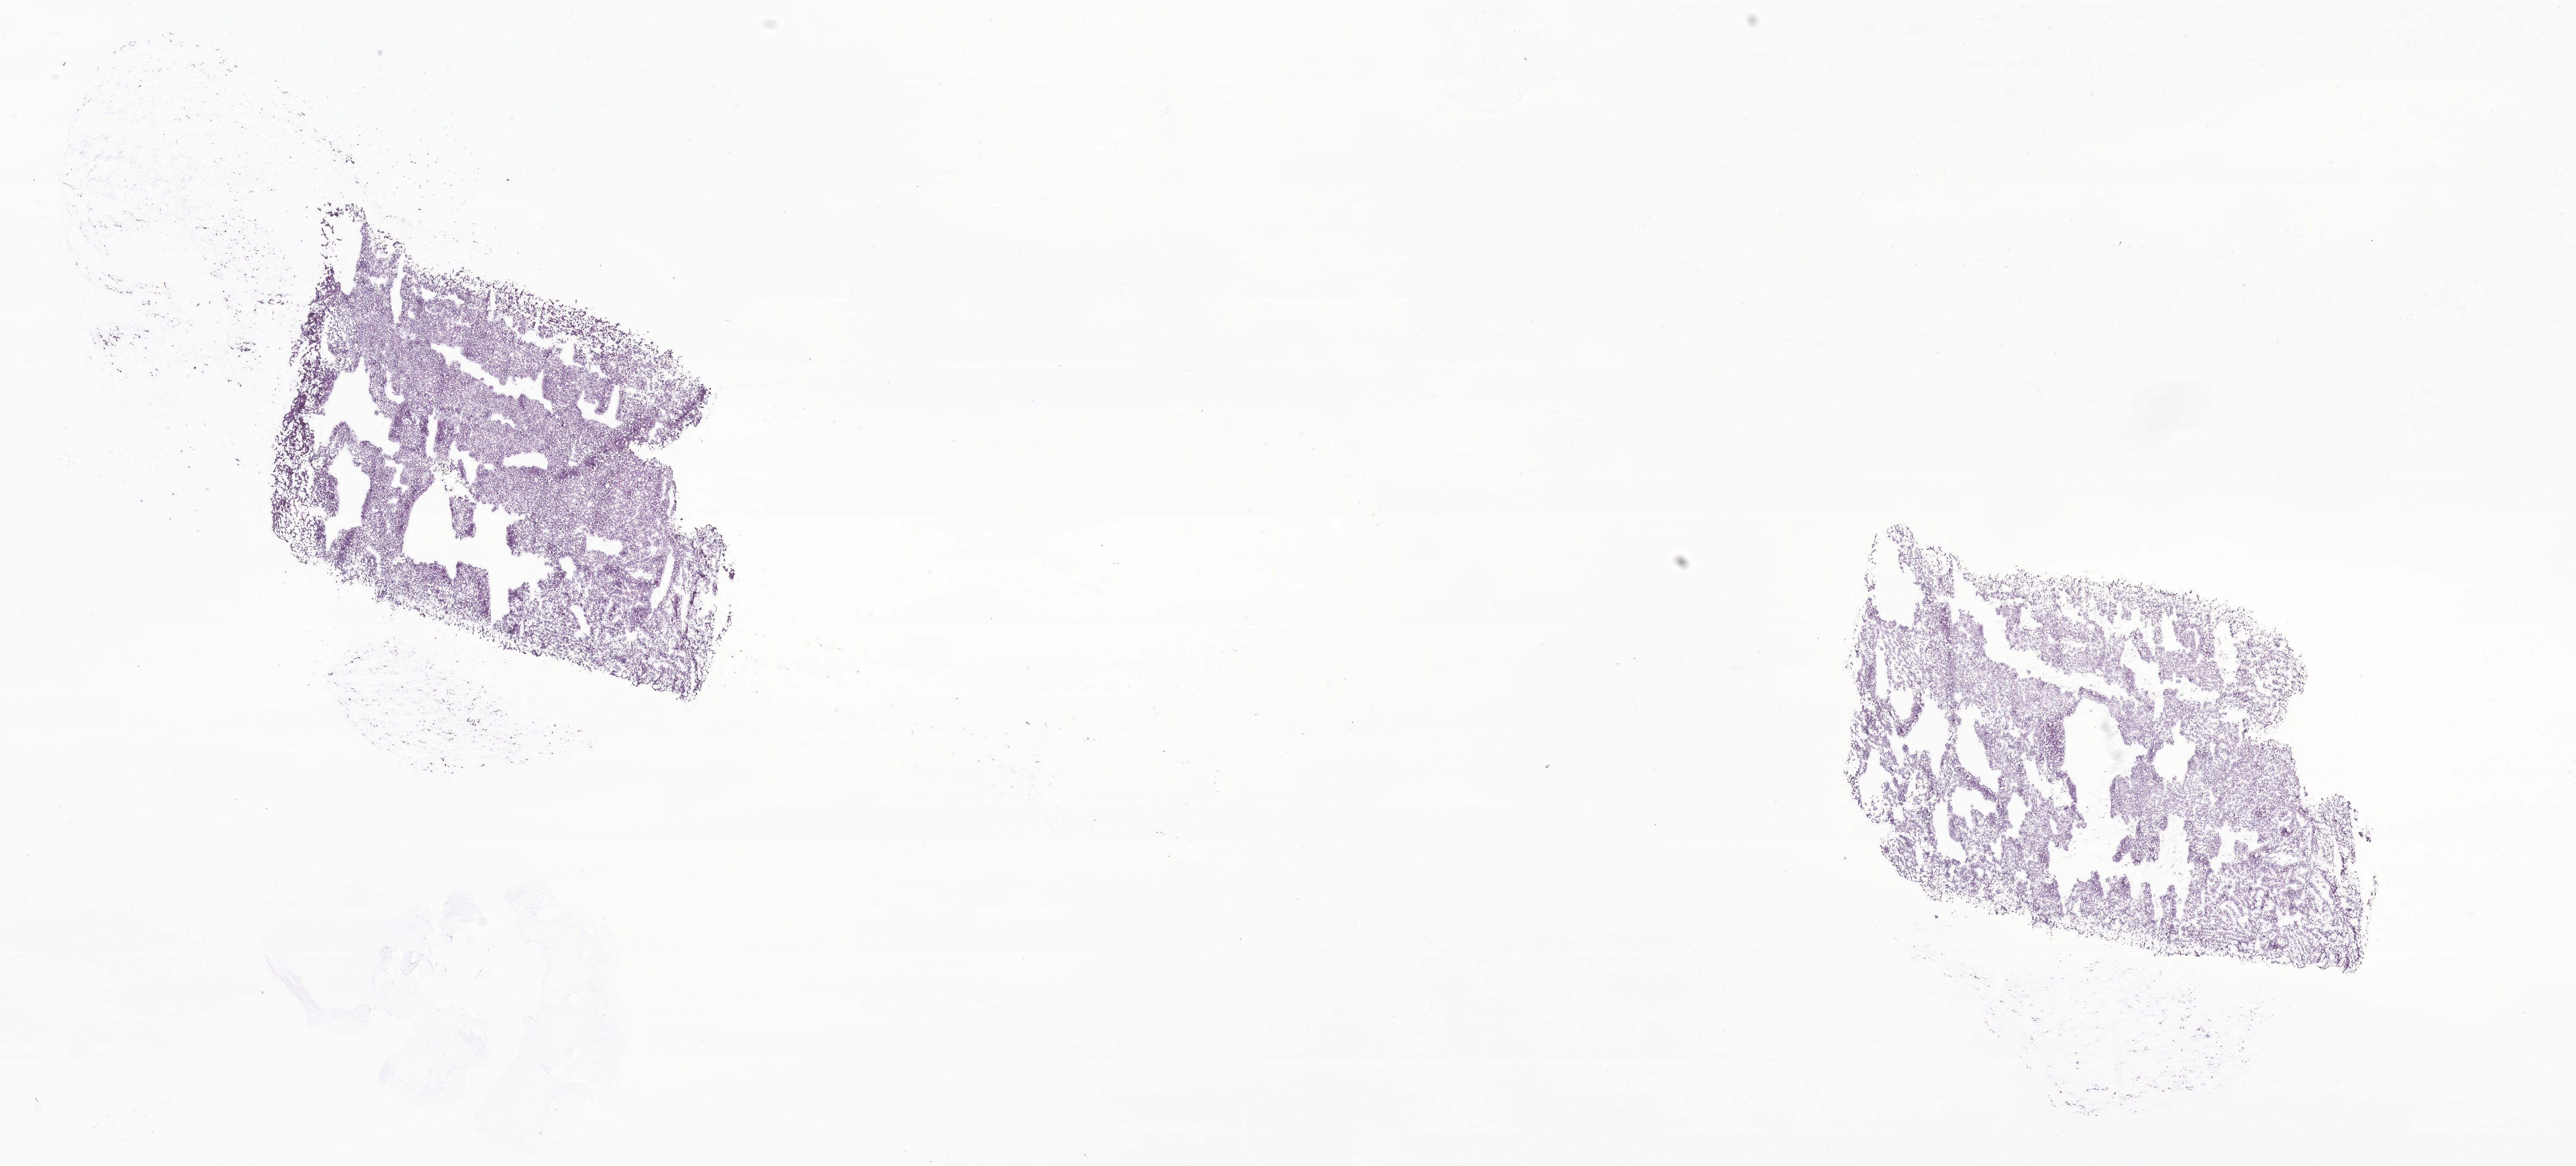
Digitized hematoxylin and eosin (H&E)-stained section of tumor tissue from the brain, a low-resolution overview of the entire scanned area, about 25.3 x 11.4 mm, frozen section (OCT-embedded). Male patient, age 57 months (4 years 9 months).
- recorded diagnosis: Medulloblastoma, NOS